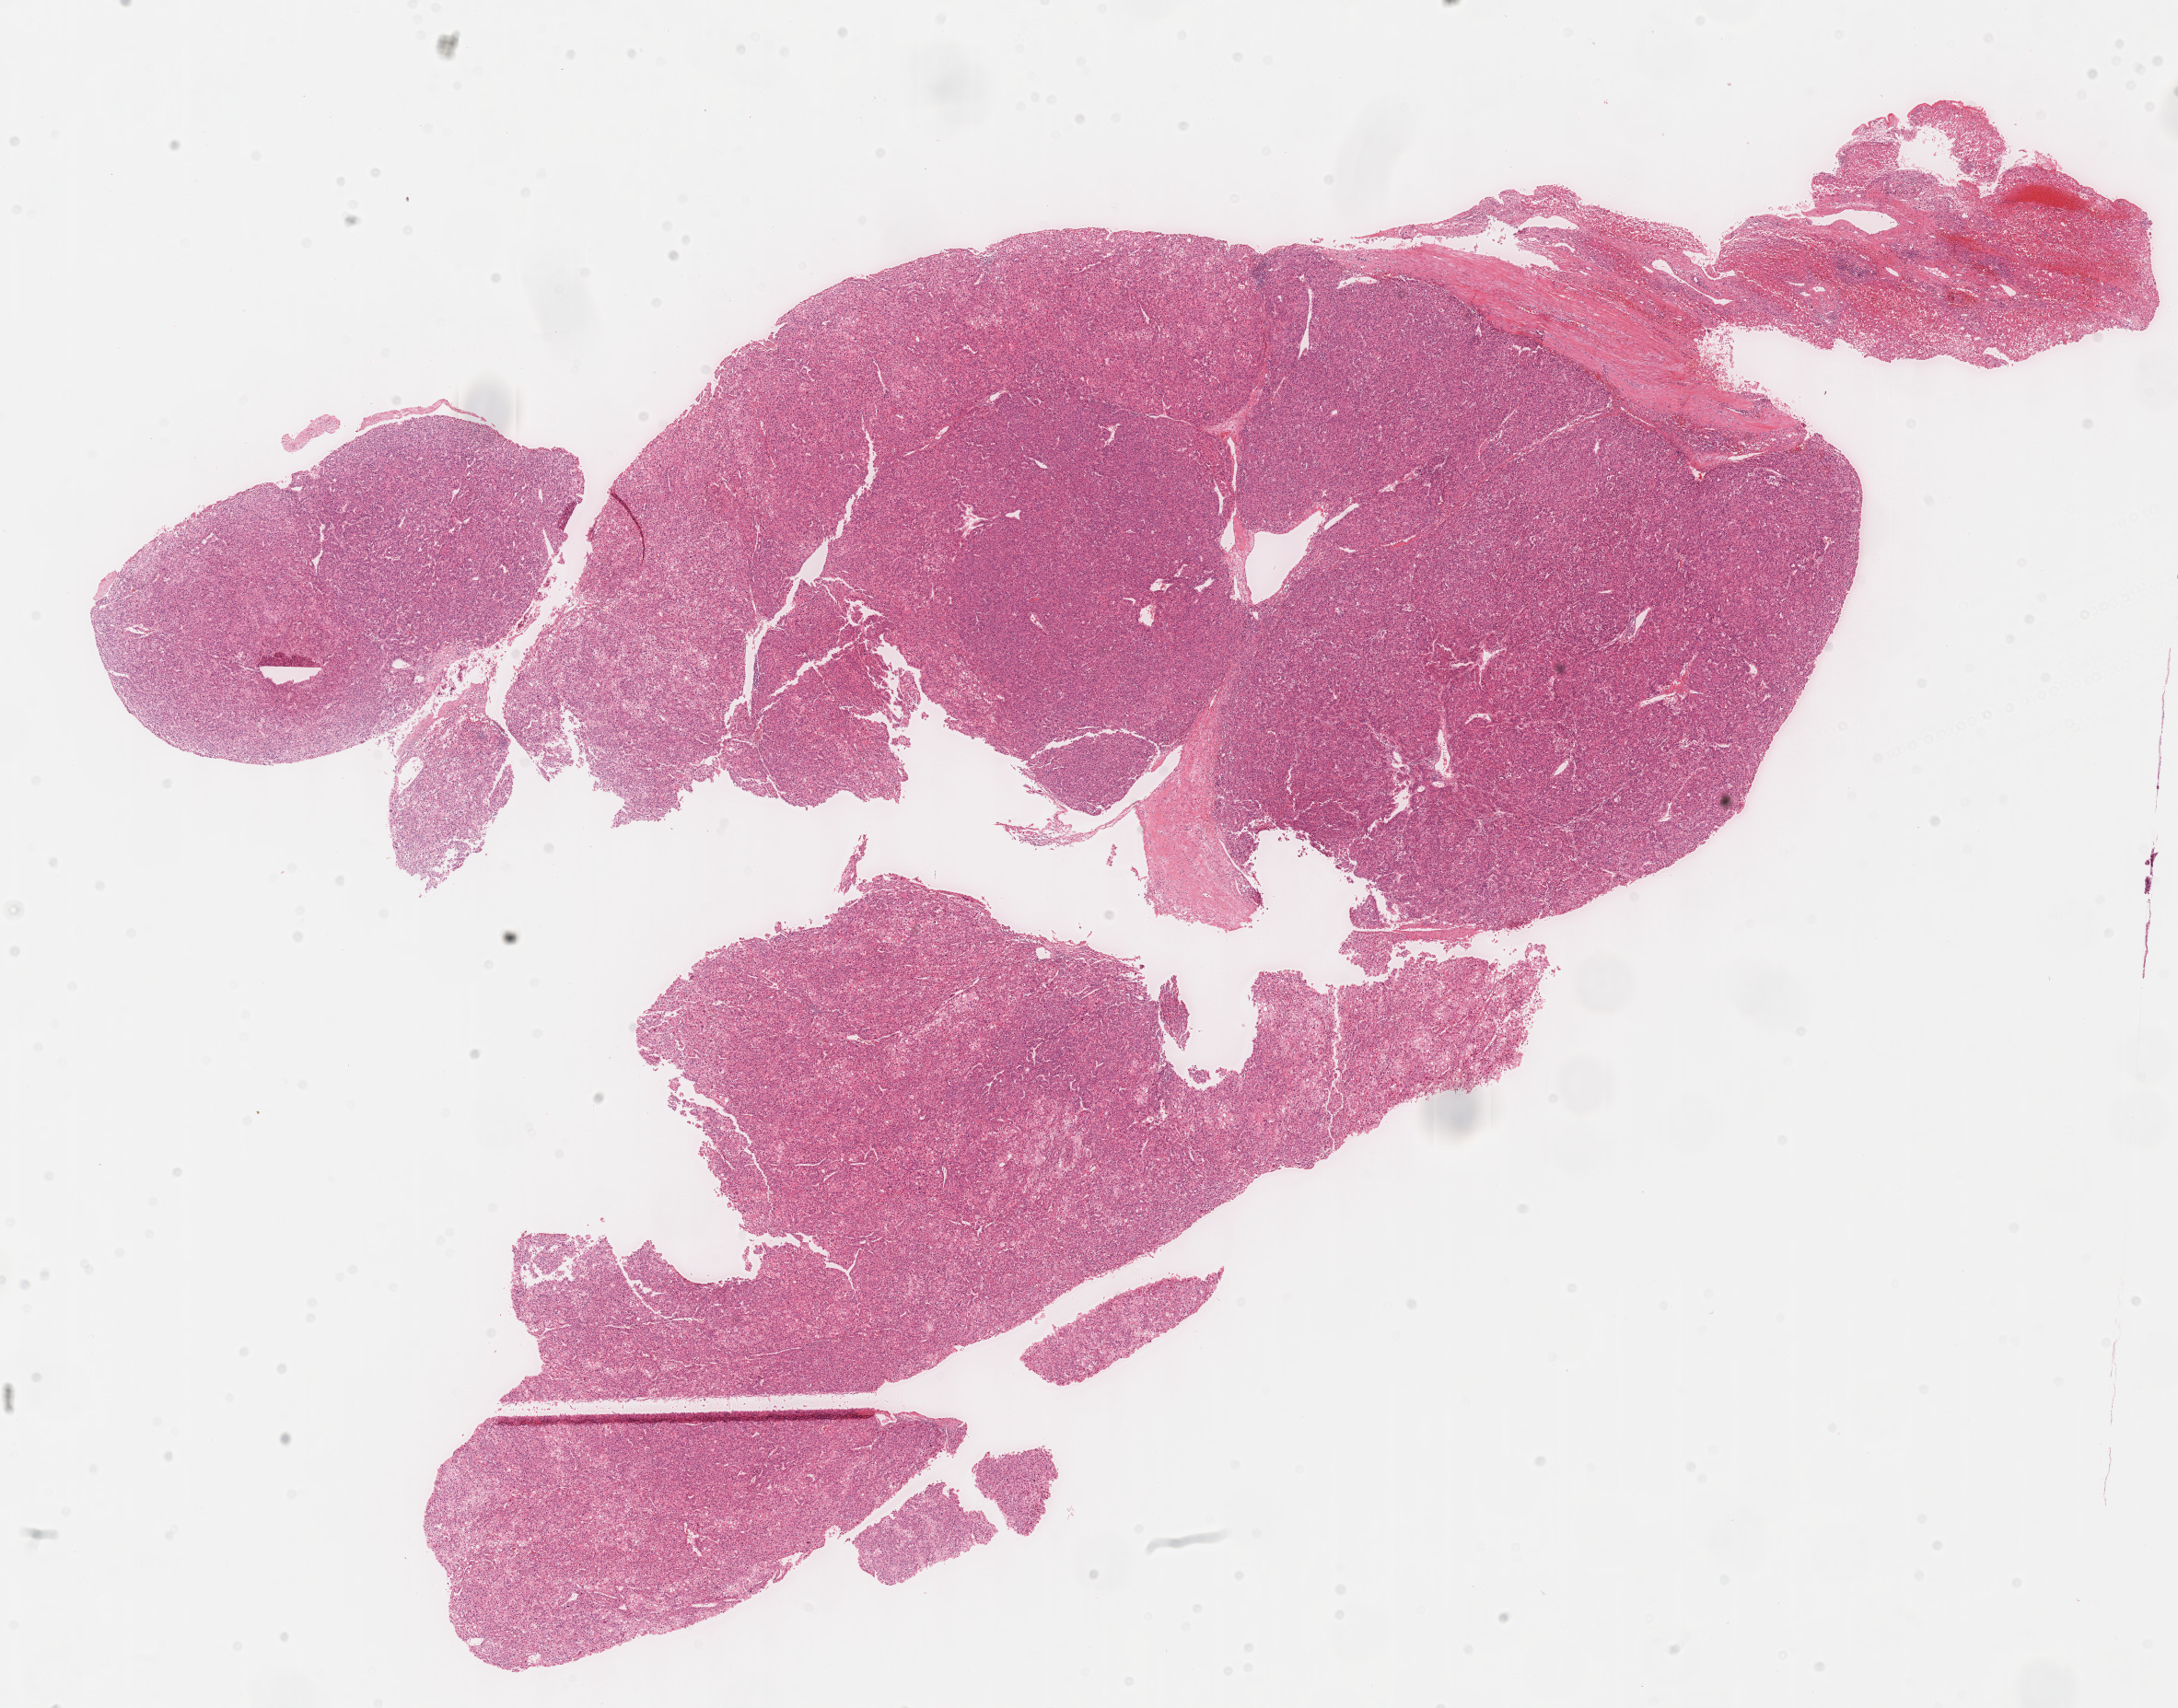
Digitized H&E tissue section (whole slide) — low-resolution overview of the scanned area, about 19.1 x 15.0 mm, formalin-fixed paraffin-embedded (FFPE) diagnostic section, primary tumour sample from the liver. Male, age 51 years at initial diagnosis. Histologic grade: G4 (undifferentiated).
AJCC pathologic stage: I. Pathologic diagnosis: Hepatocellular carcinoma, NOS.